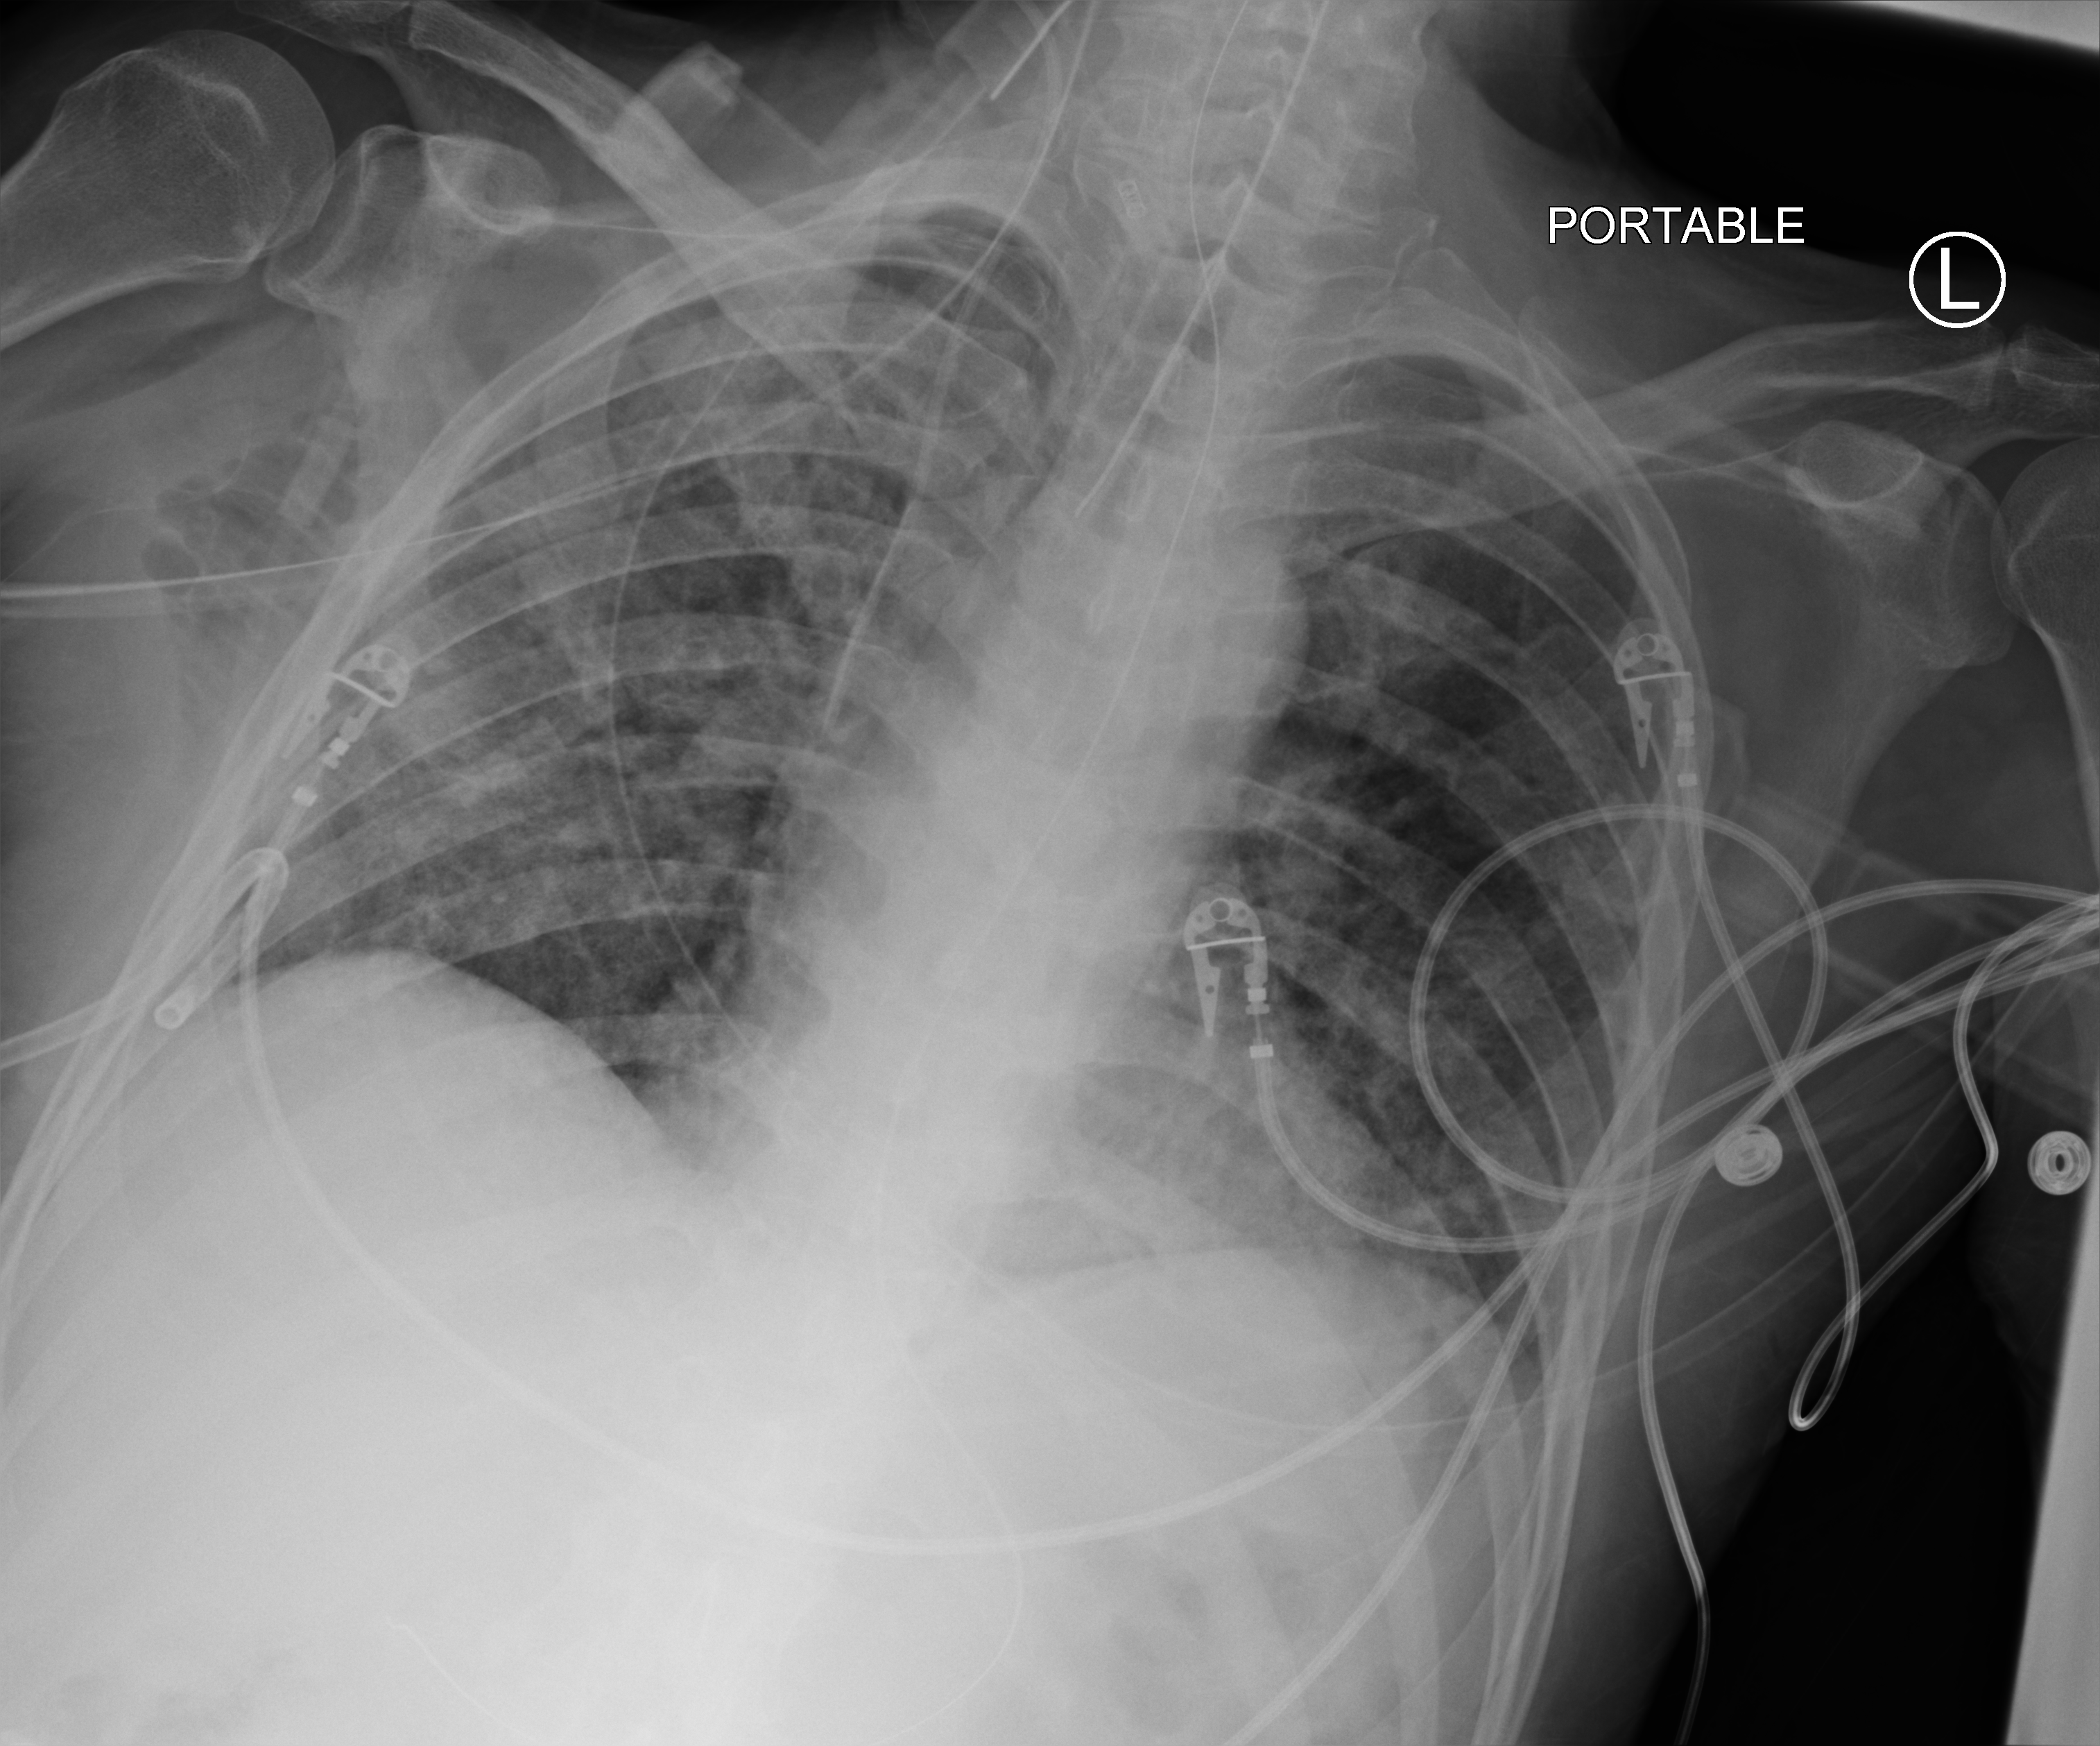
Chest X-ray (portable); anteroposterior (AP) projection. Patient hospitalised with COVID-19; male, aged 18–59 years.
Admission-level facts for this patient (not findings on this image; timing relative to this image not recorded): COPD (admission record): no.